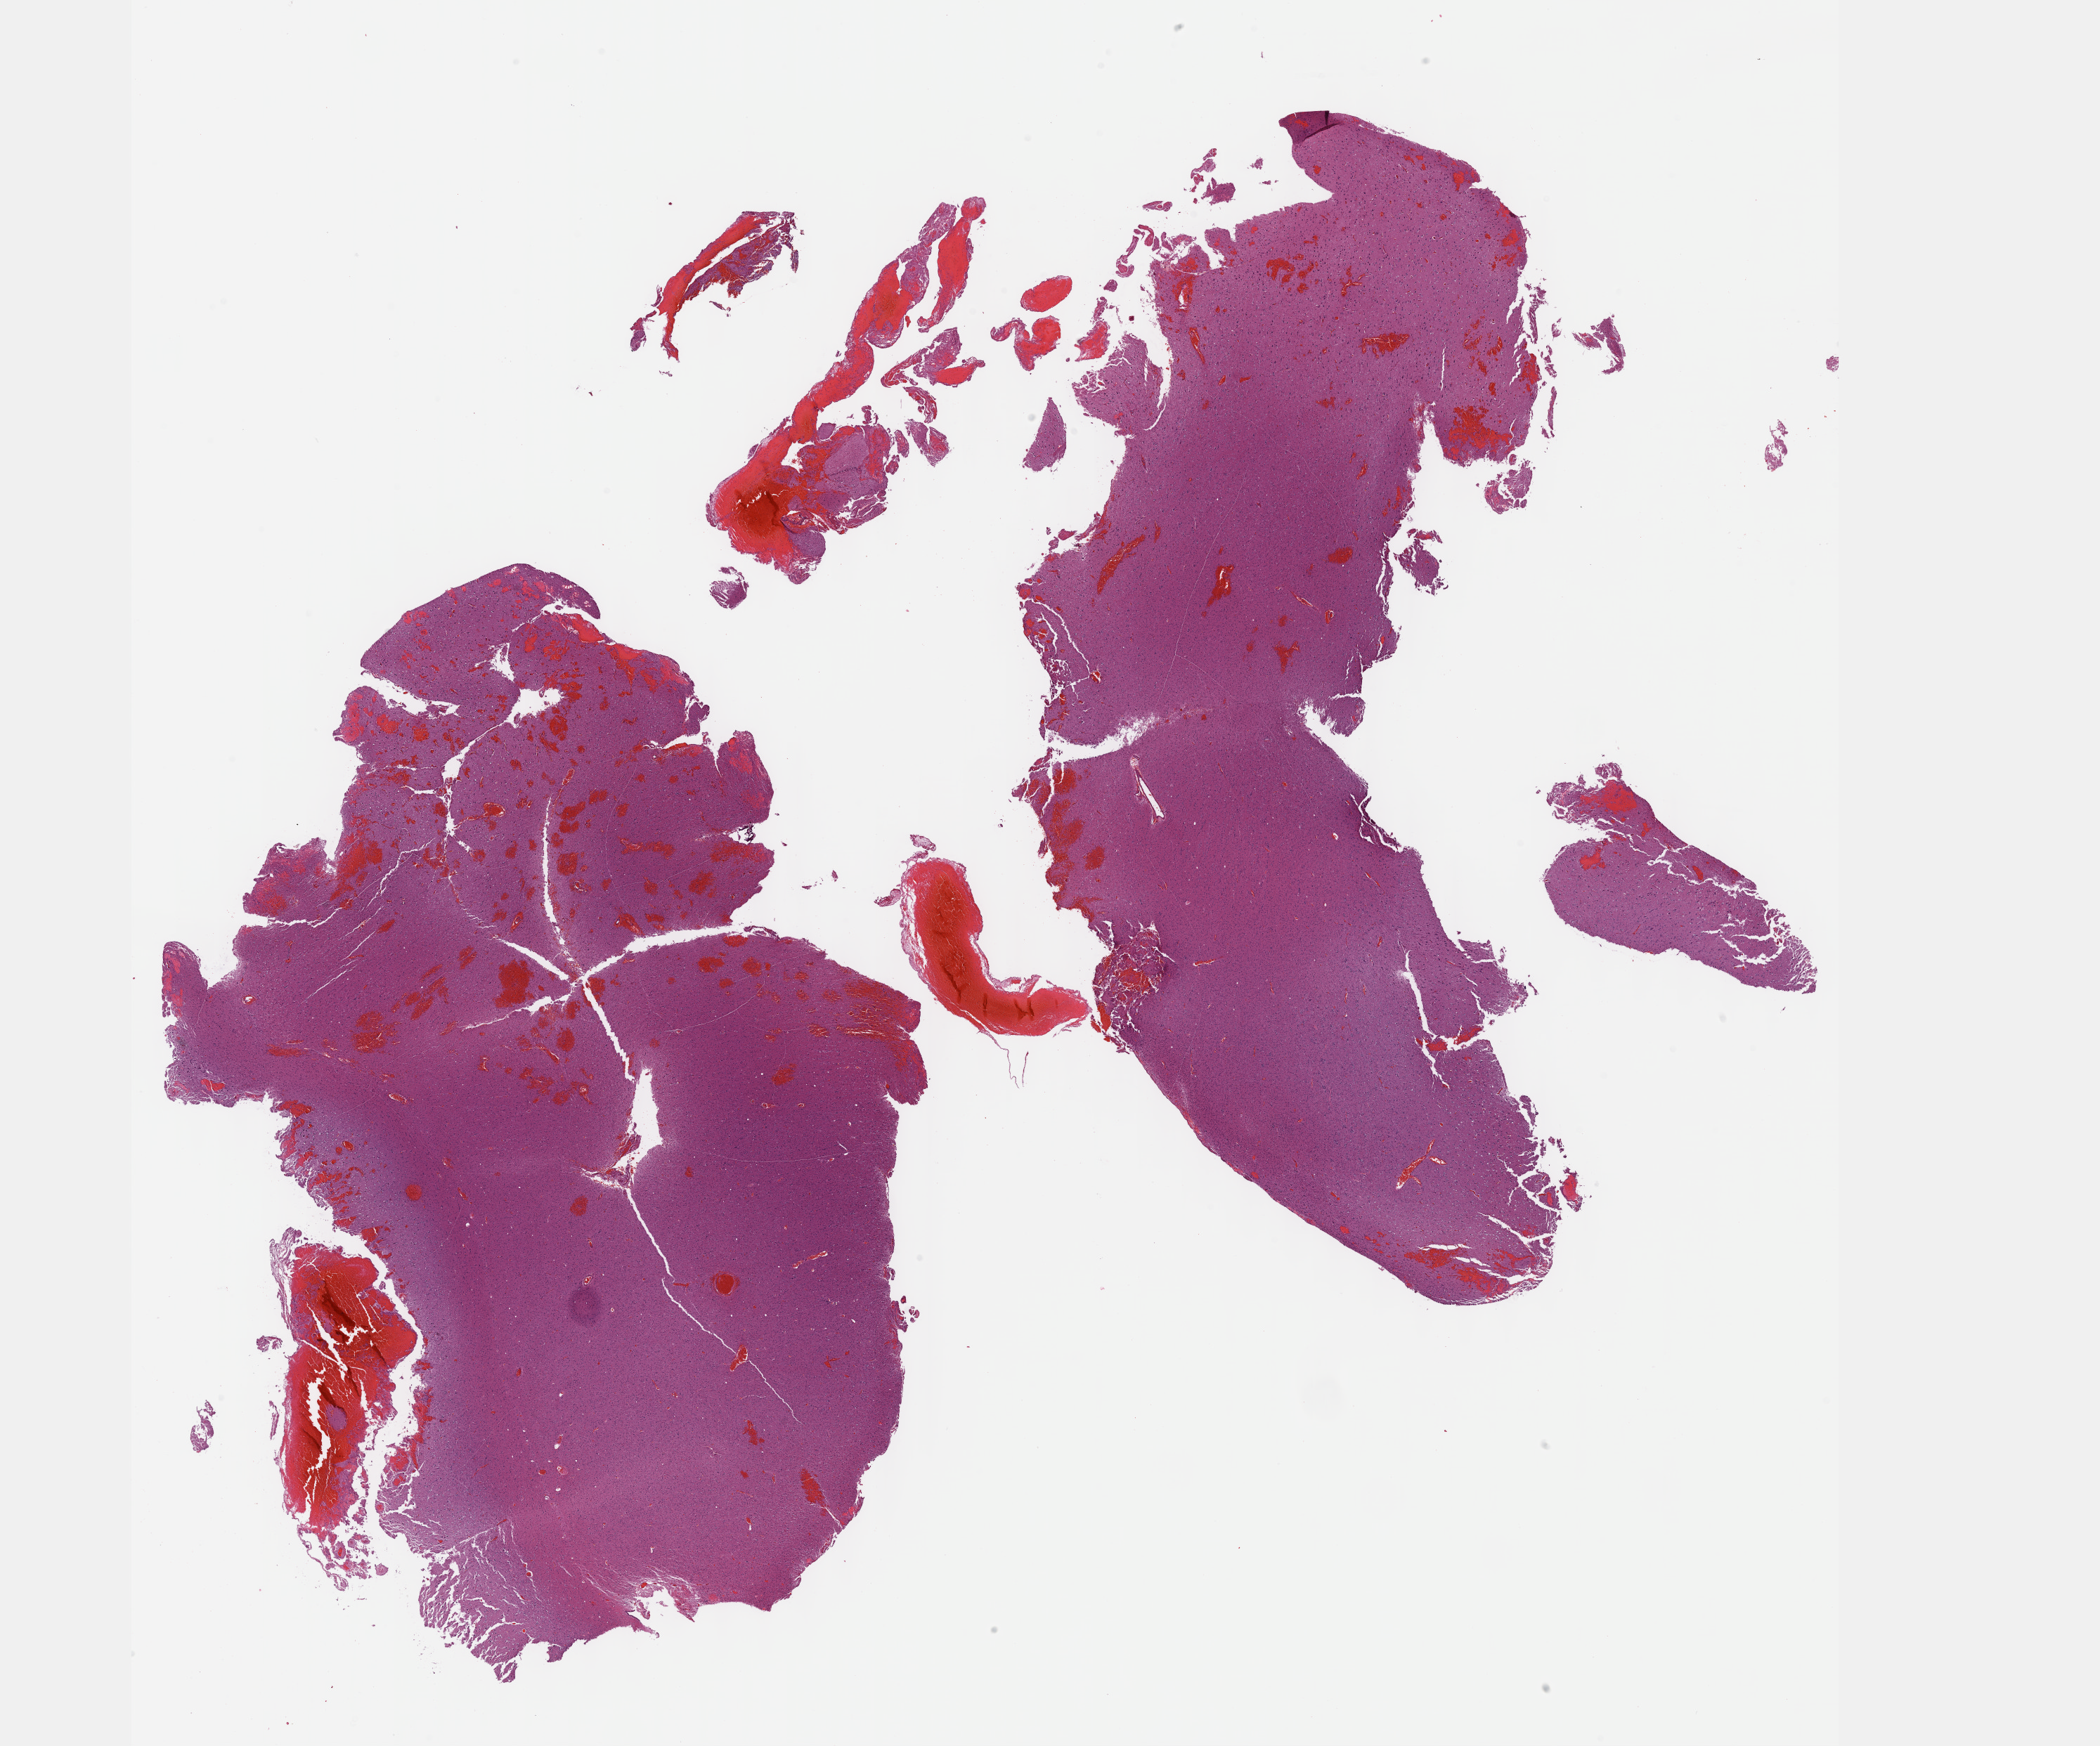
H&E-stained whole-slide image — whole scanned area (about 24.1 x 20.1 mm, from a 40x scan) shown as a low-resolution overview; formalin-fixed paraffin-embedded (FFPE) diagnostic section; sample: primary tumour, brain. Male patient; age at initial diagnosis 38 years. Histologic grade: G2 (moderately differentiated).
• laterality: left
• pathologic diagnosis: Oligodendroglioma, NOS (cerebrum)